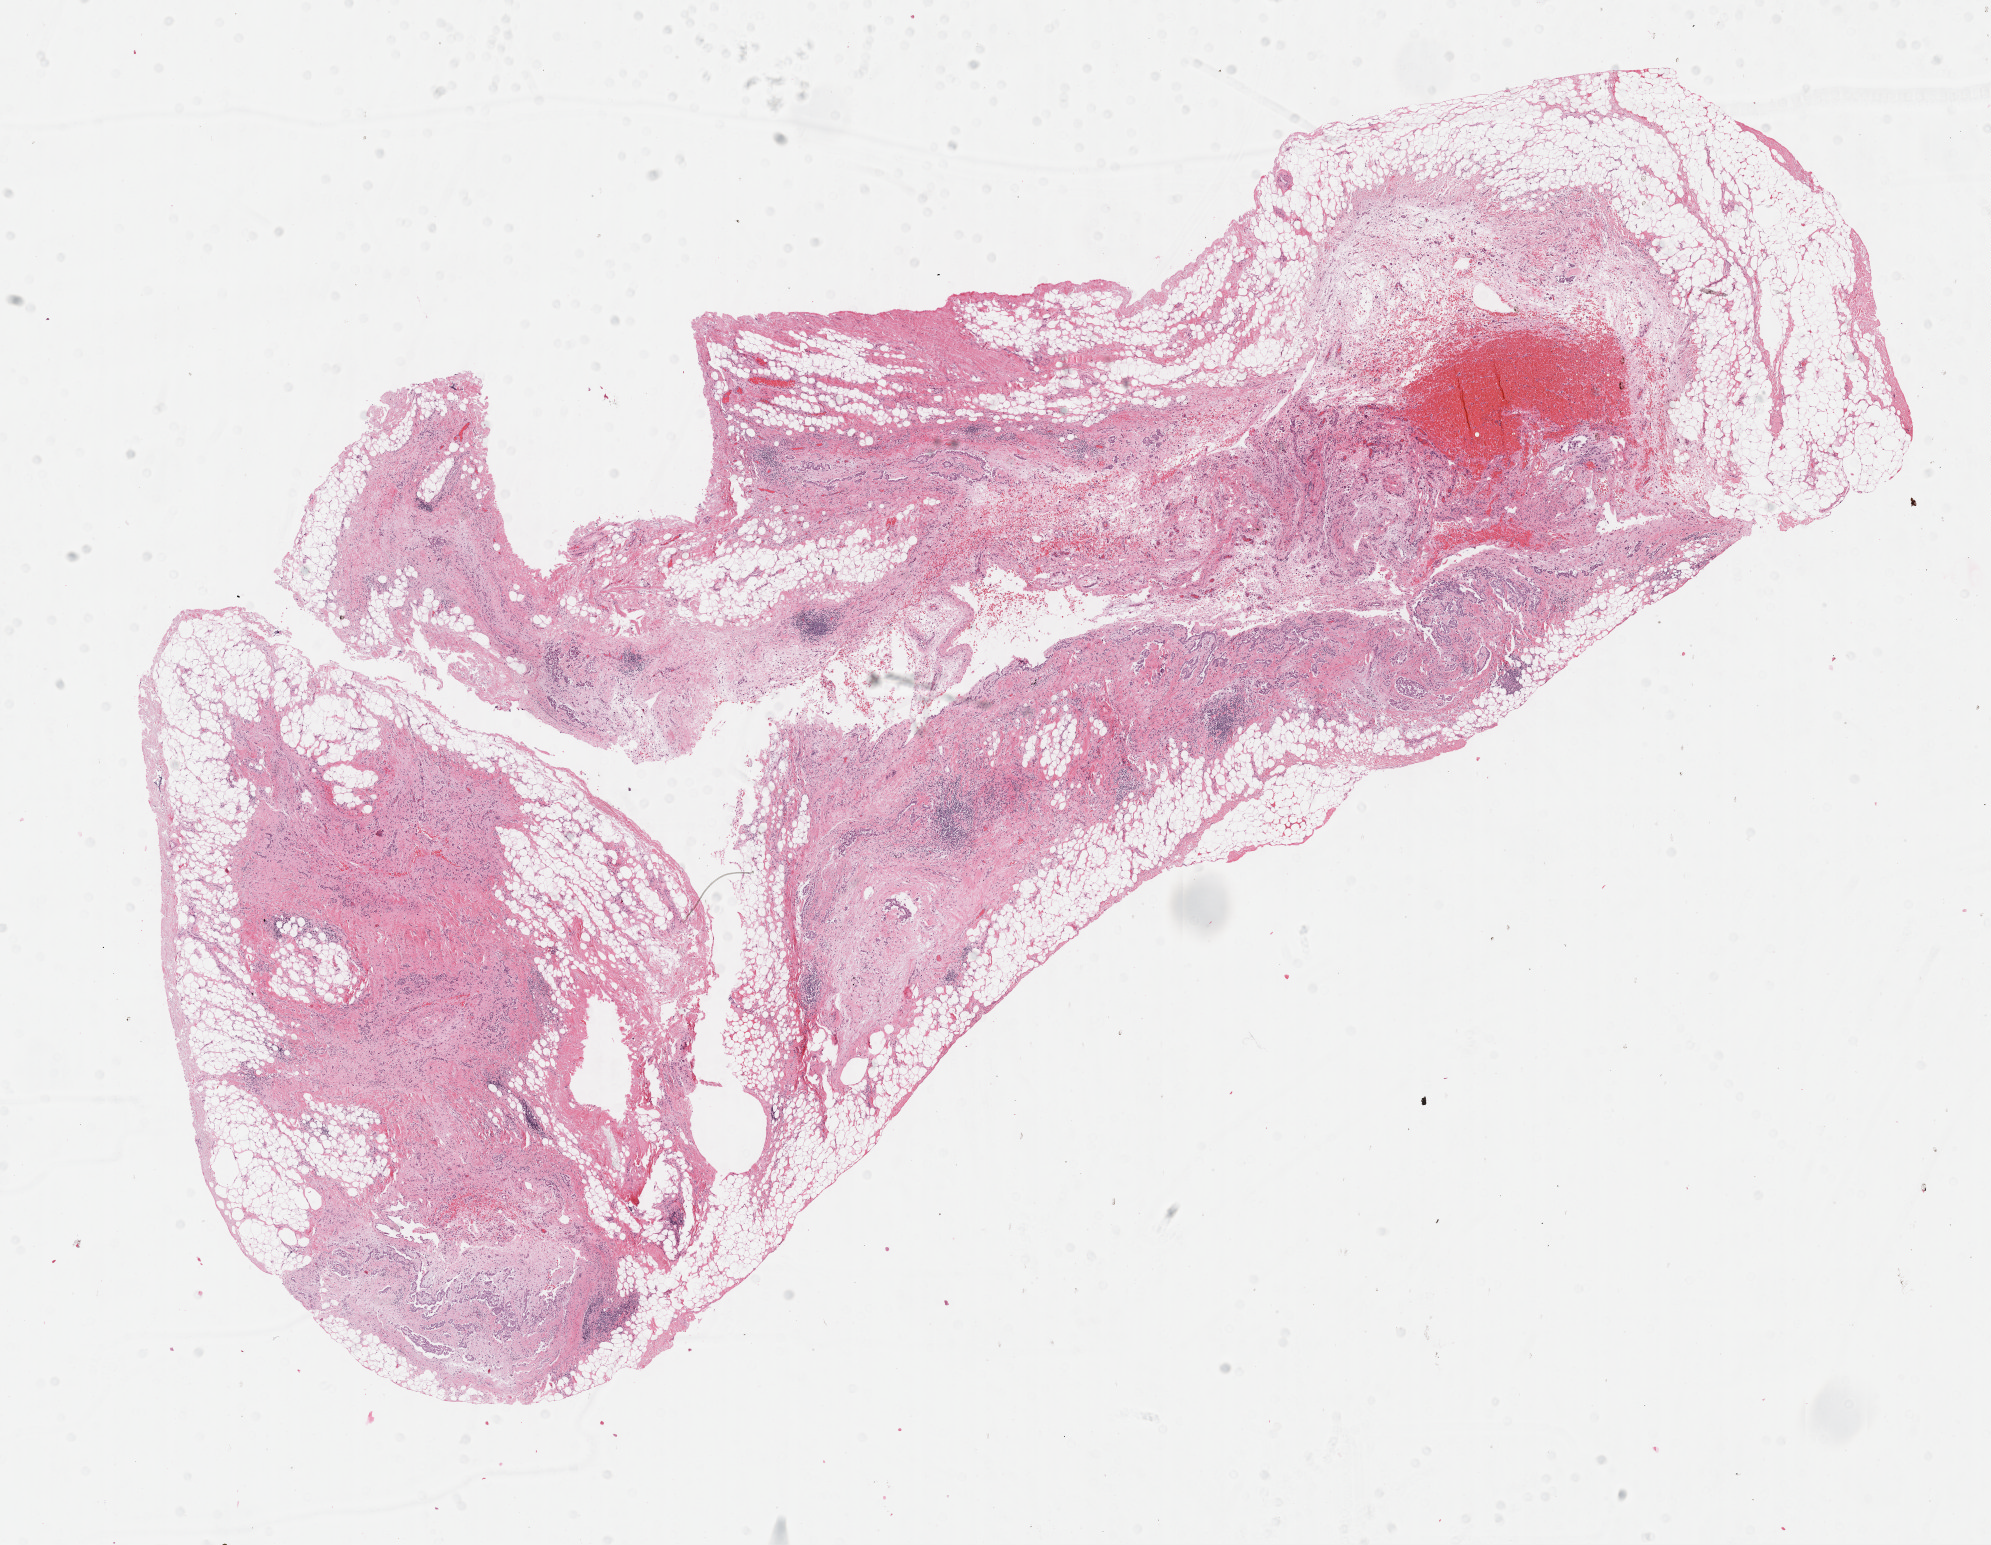
Whole-slide histology image, Hematoxylin and eosin (H&E) stained — shown as a low-resolution overview of the whole scanned area (about 16.1 x 12.5 mm, acquisition: 40x scan), formalin-fixed paraffin-embedded (FFPE) diagnostic section, mesothelium, primary tumour sample. Male patient; age at initial diagnosis 77 years.
Diagnosis: Epithelioid mesothelioma, malignant (pleura, NOS).